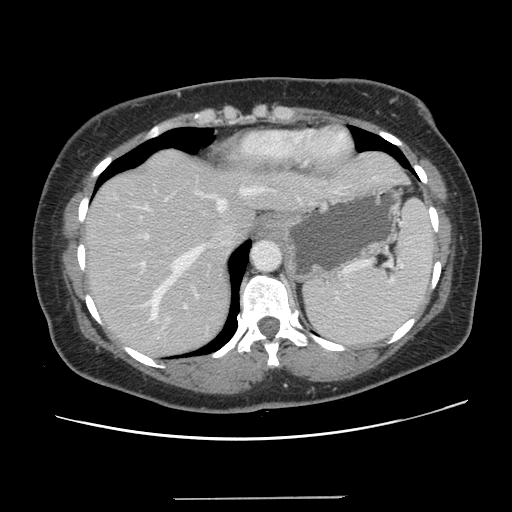
Contrast-enhanced abdominal CT, one axial slice. Position 106 of 141 along the scan axis. Intravenous contrast given. Soft-tissue window (W 400 / L 40 HU). 512 × 512 image matrix, field of view 366 × 366 mm. Female patient, age 53 years. Case-level facts recorded for this patient, not image findings: diagnosis: colorectal cancer liver metastases, imaged before liver resection; multiple liver metastases: no; largest metastasis: 14.5 cm; chemotherapy before resection: yes.
Outlined on this slice (outlined manually by an expert reader):
- hepatic veins: bounding box (x1, y1, x2, y2) in pixels: (113, 184, 277, 320)
- liver: (85, 149, 406, 358)
- planned liver remnant (the part of the liver to remain after resection): (85, 208, 257, 358)
- portal vein (with intrahepatic branches): (118, 197, 188, 323)